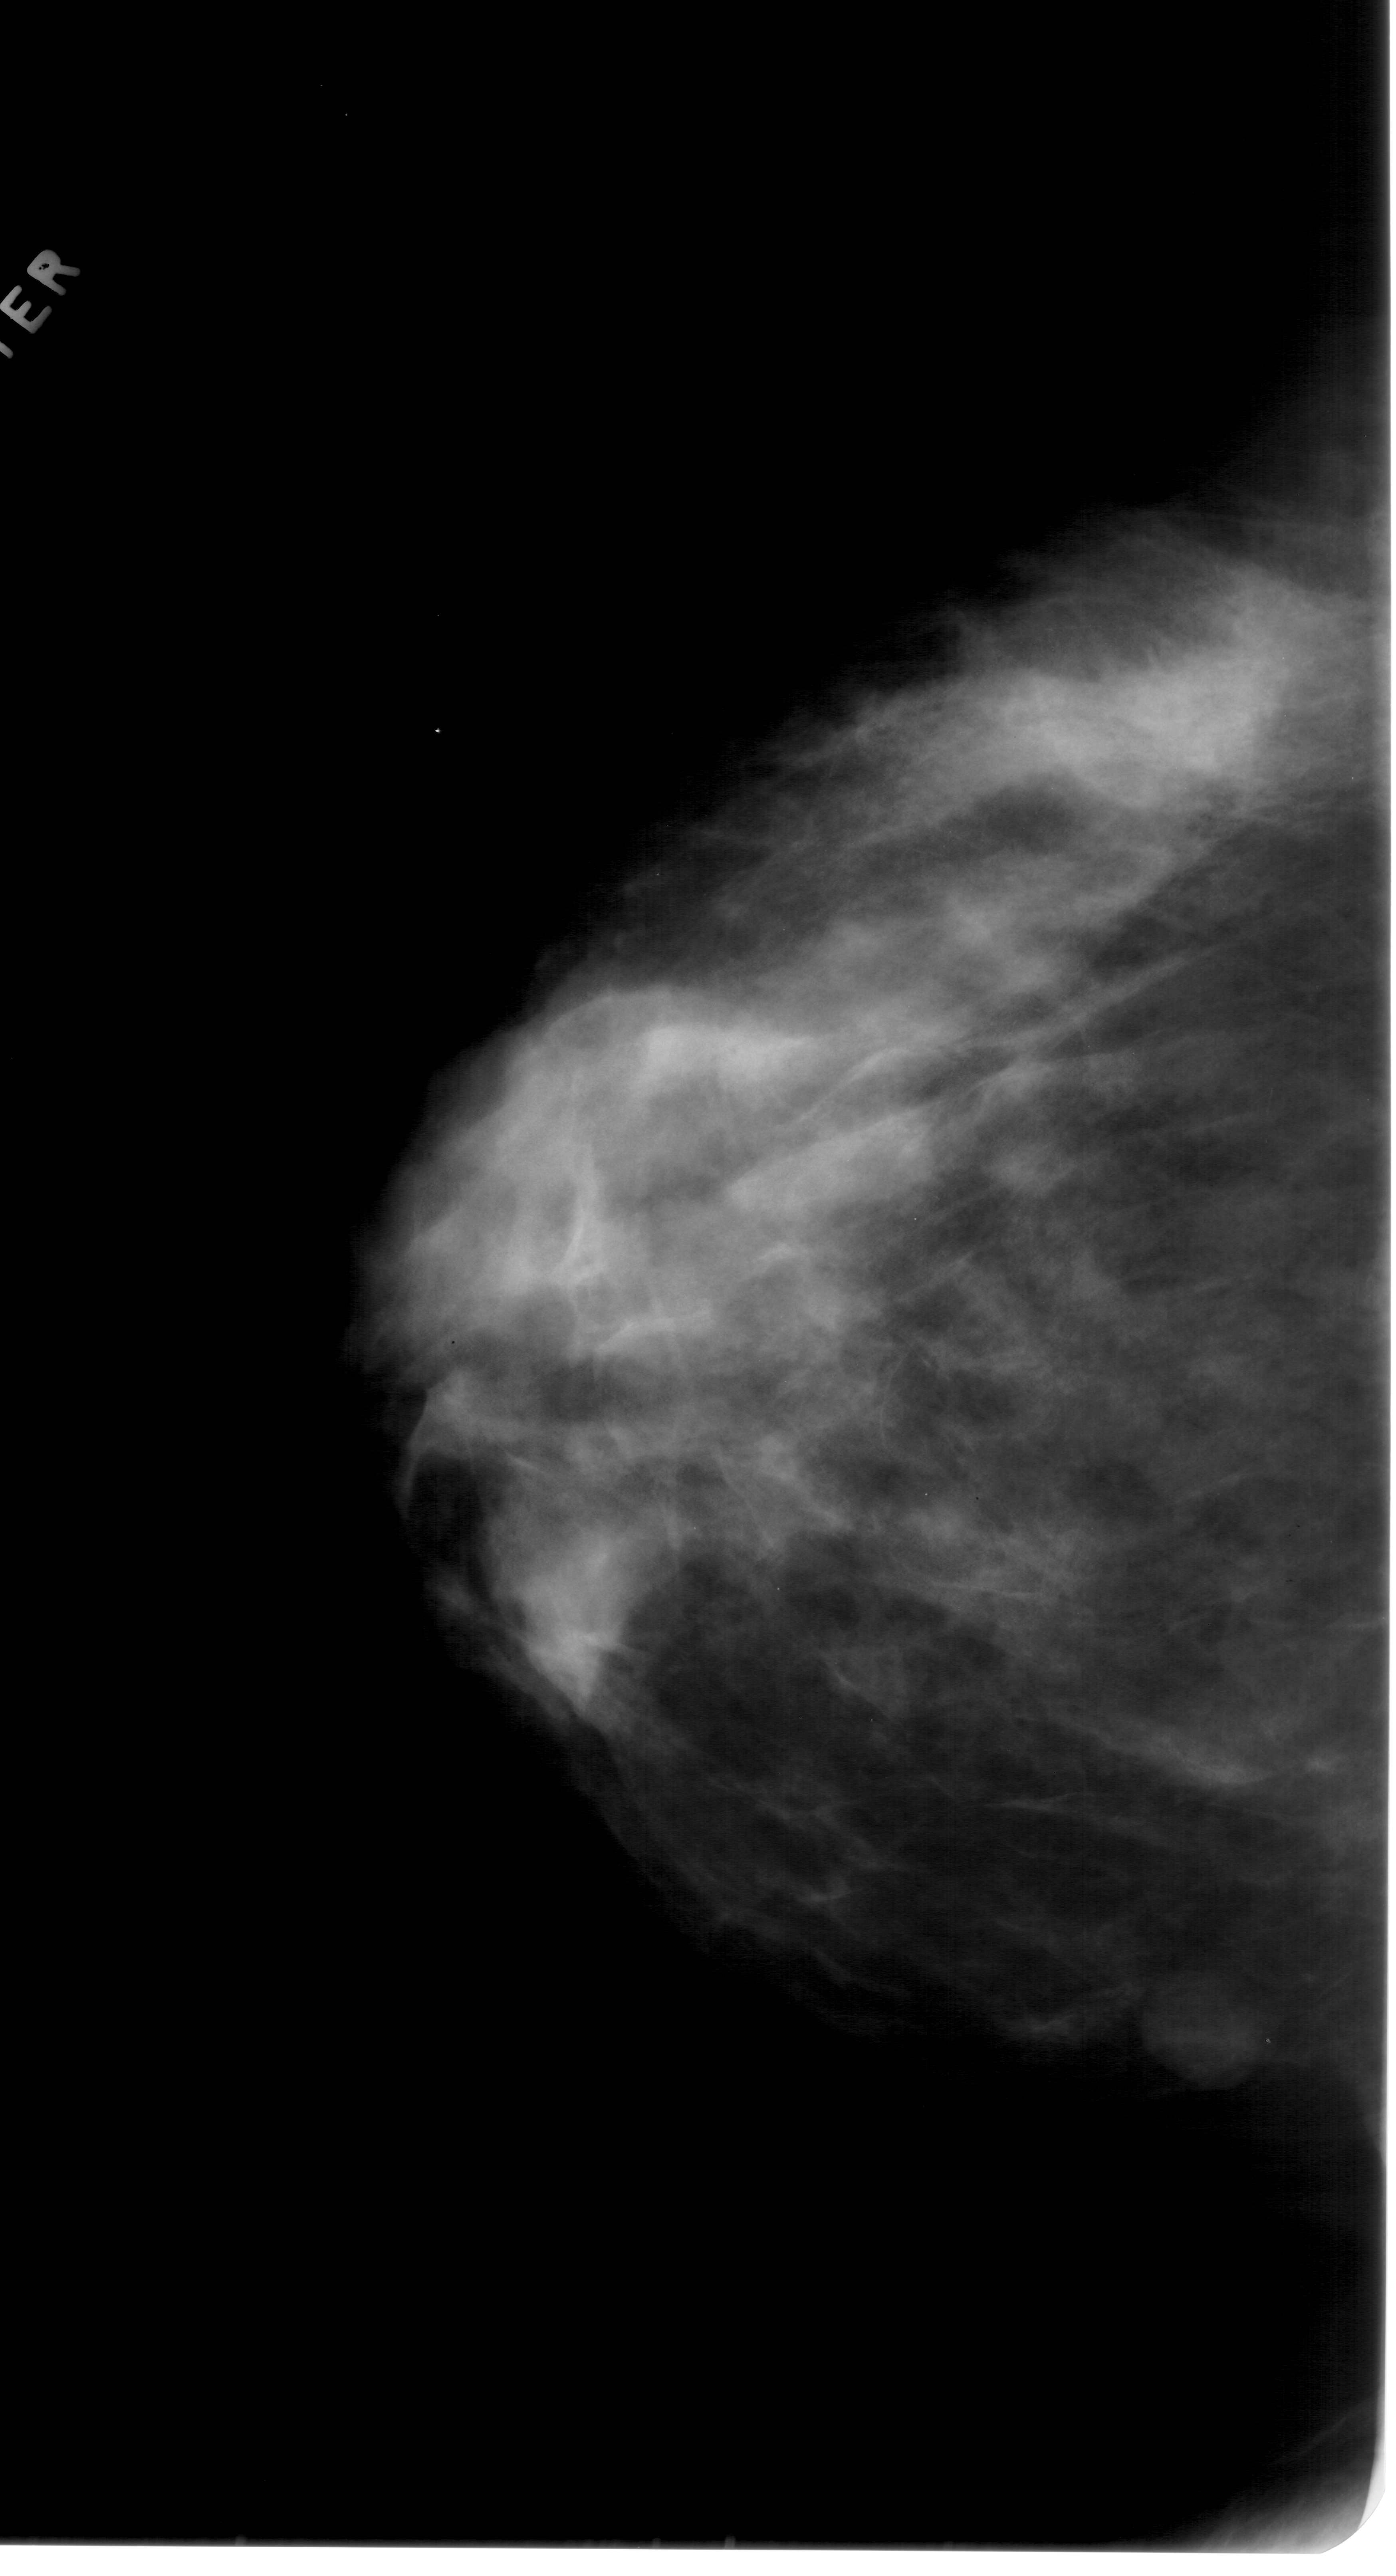
Mammogram (digitized film); left breast; CC view; breast composition: extremely dense (BI-RADS density category 4 of 4).
Finding: mass, shape oval, margins circumscribed; BI-RADS assessment category 3; pathology (as recorded): benign.